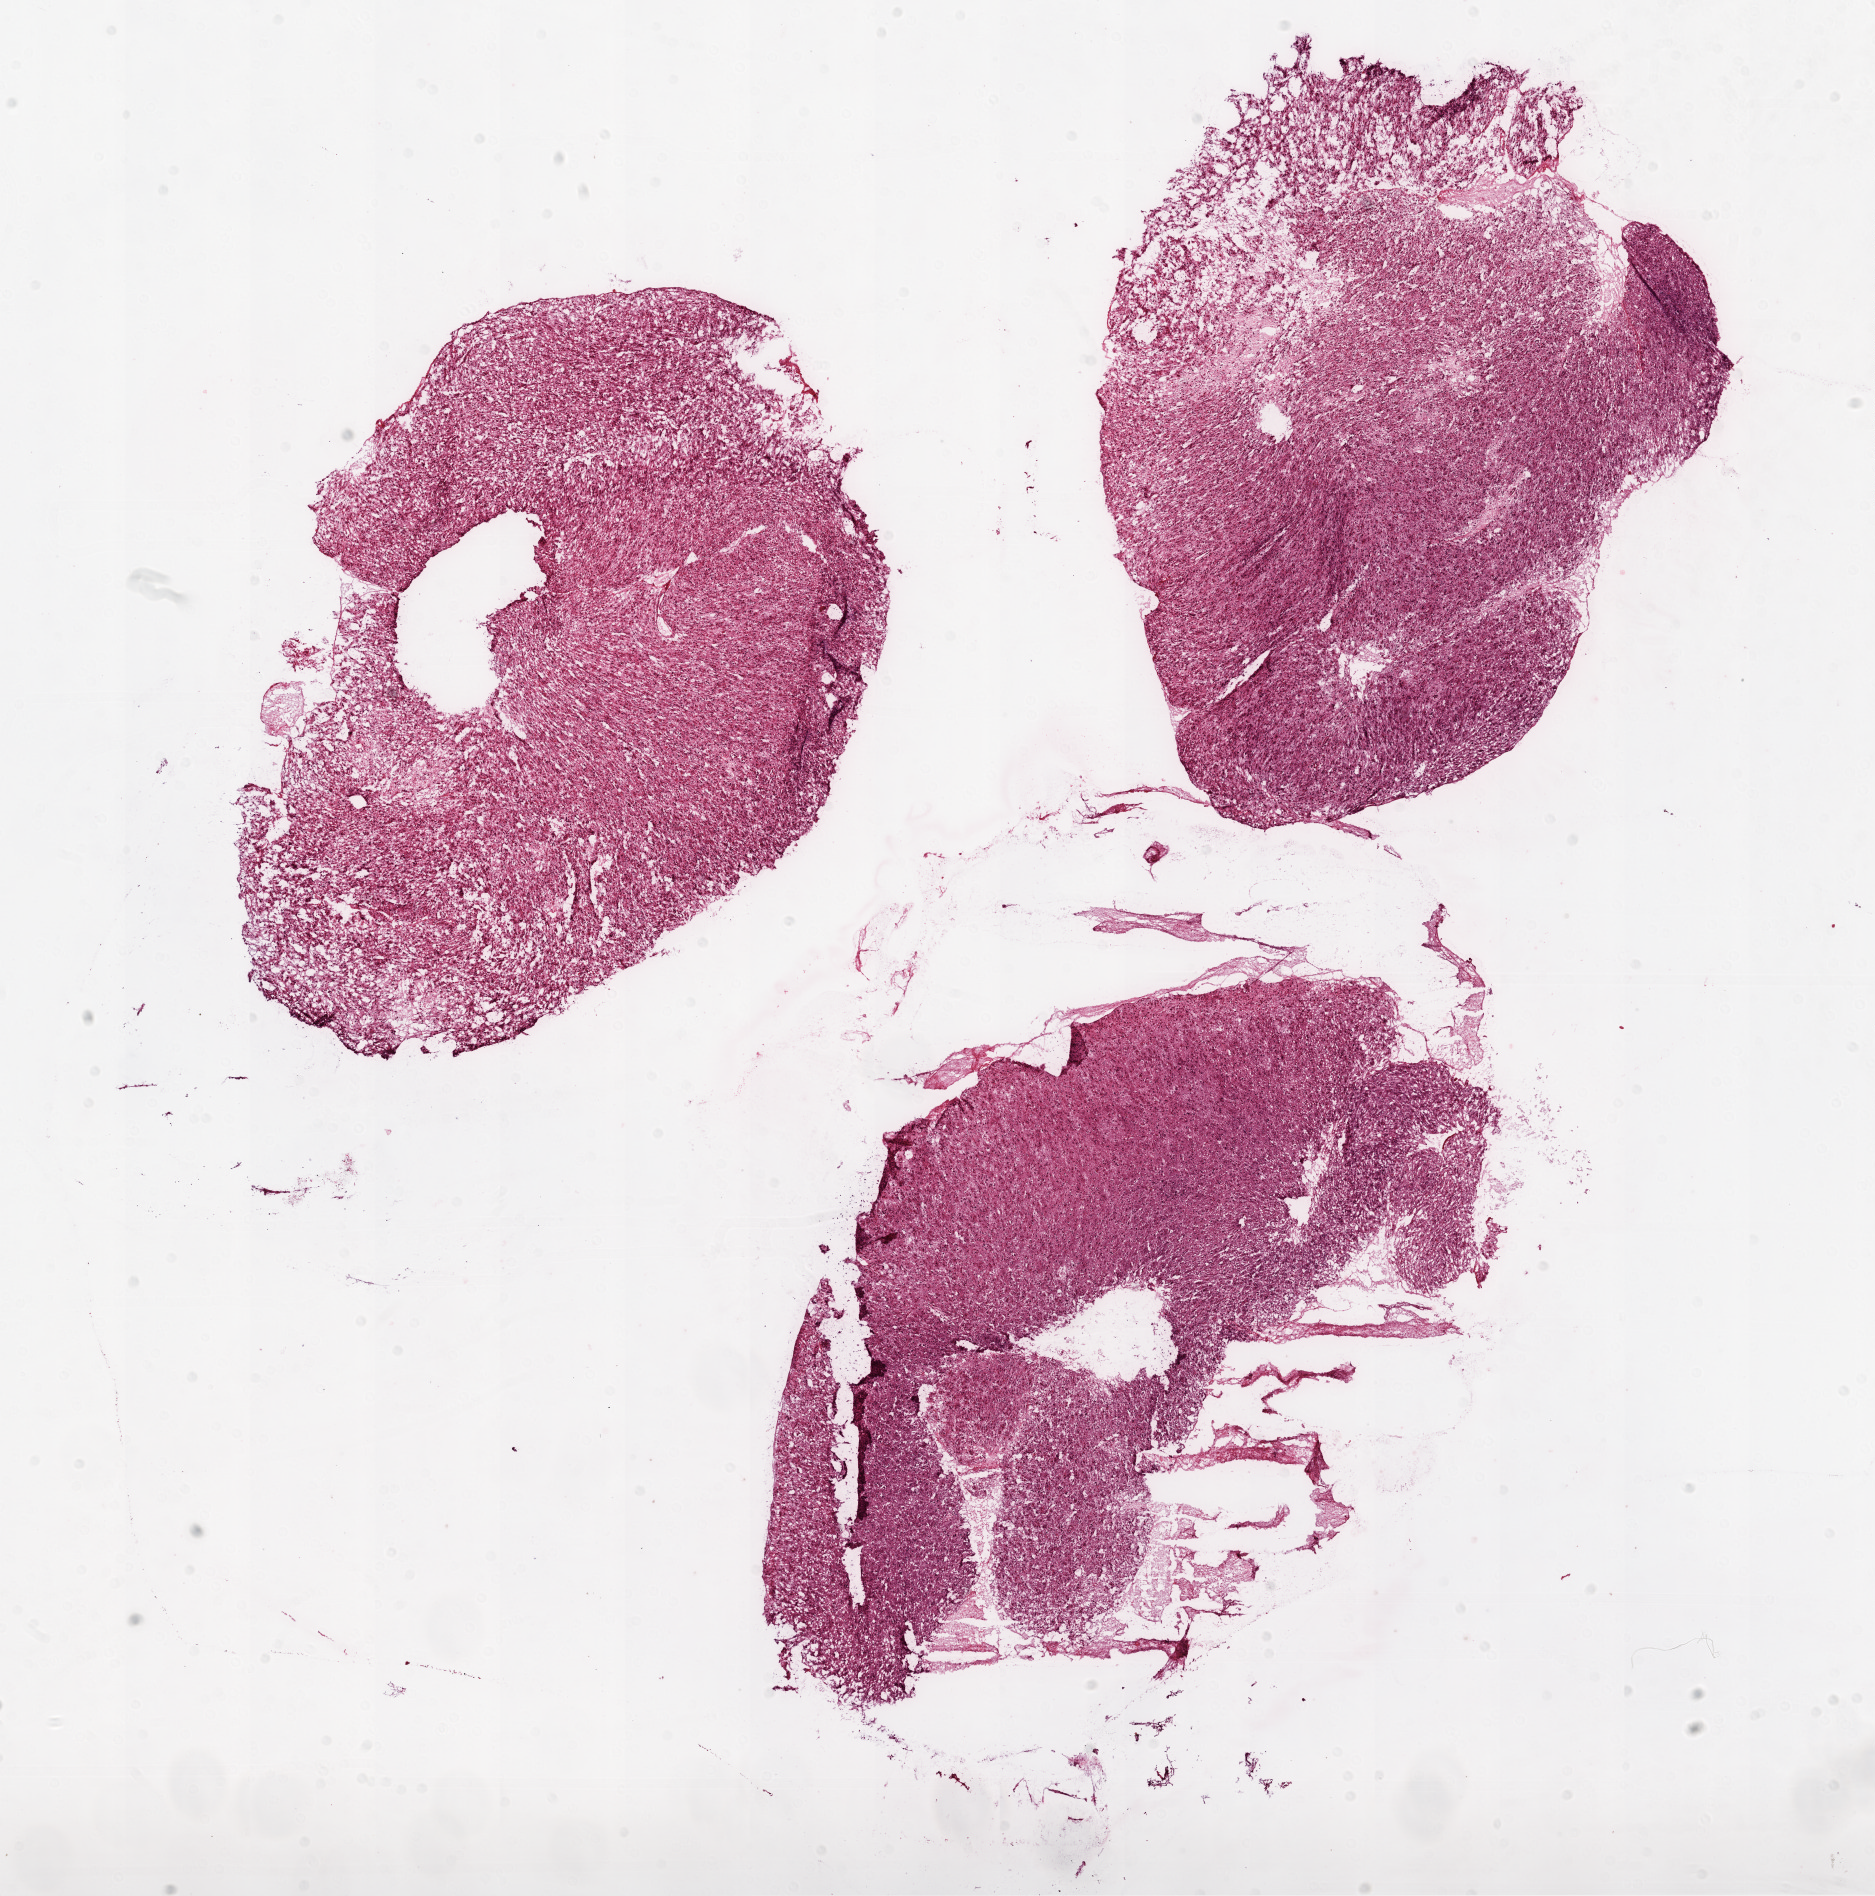
Hematoxylin and eosin (H&E) stained whole-slide image, whole scanned area (about 15.0 x 15.2 mm, acquisition: 20x scan) shown as a low-resolution overview, frozen section from the top of the tissue portion, primary tumour sample from the brain. Male, age 51 years at initial diagnosis. Composition of this section per pathologist review: tumour cells 90%, tumour nuclei 80%, normal cells 0%, stromal cells 5%, necrosis 5%.
Histologic diagnosis: Glioblastoma.